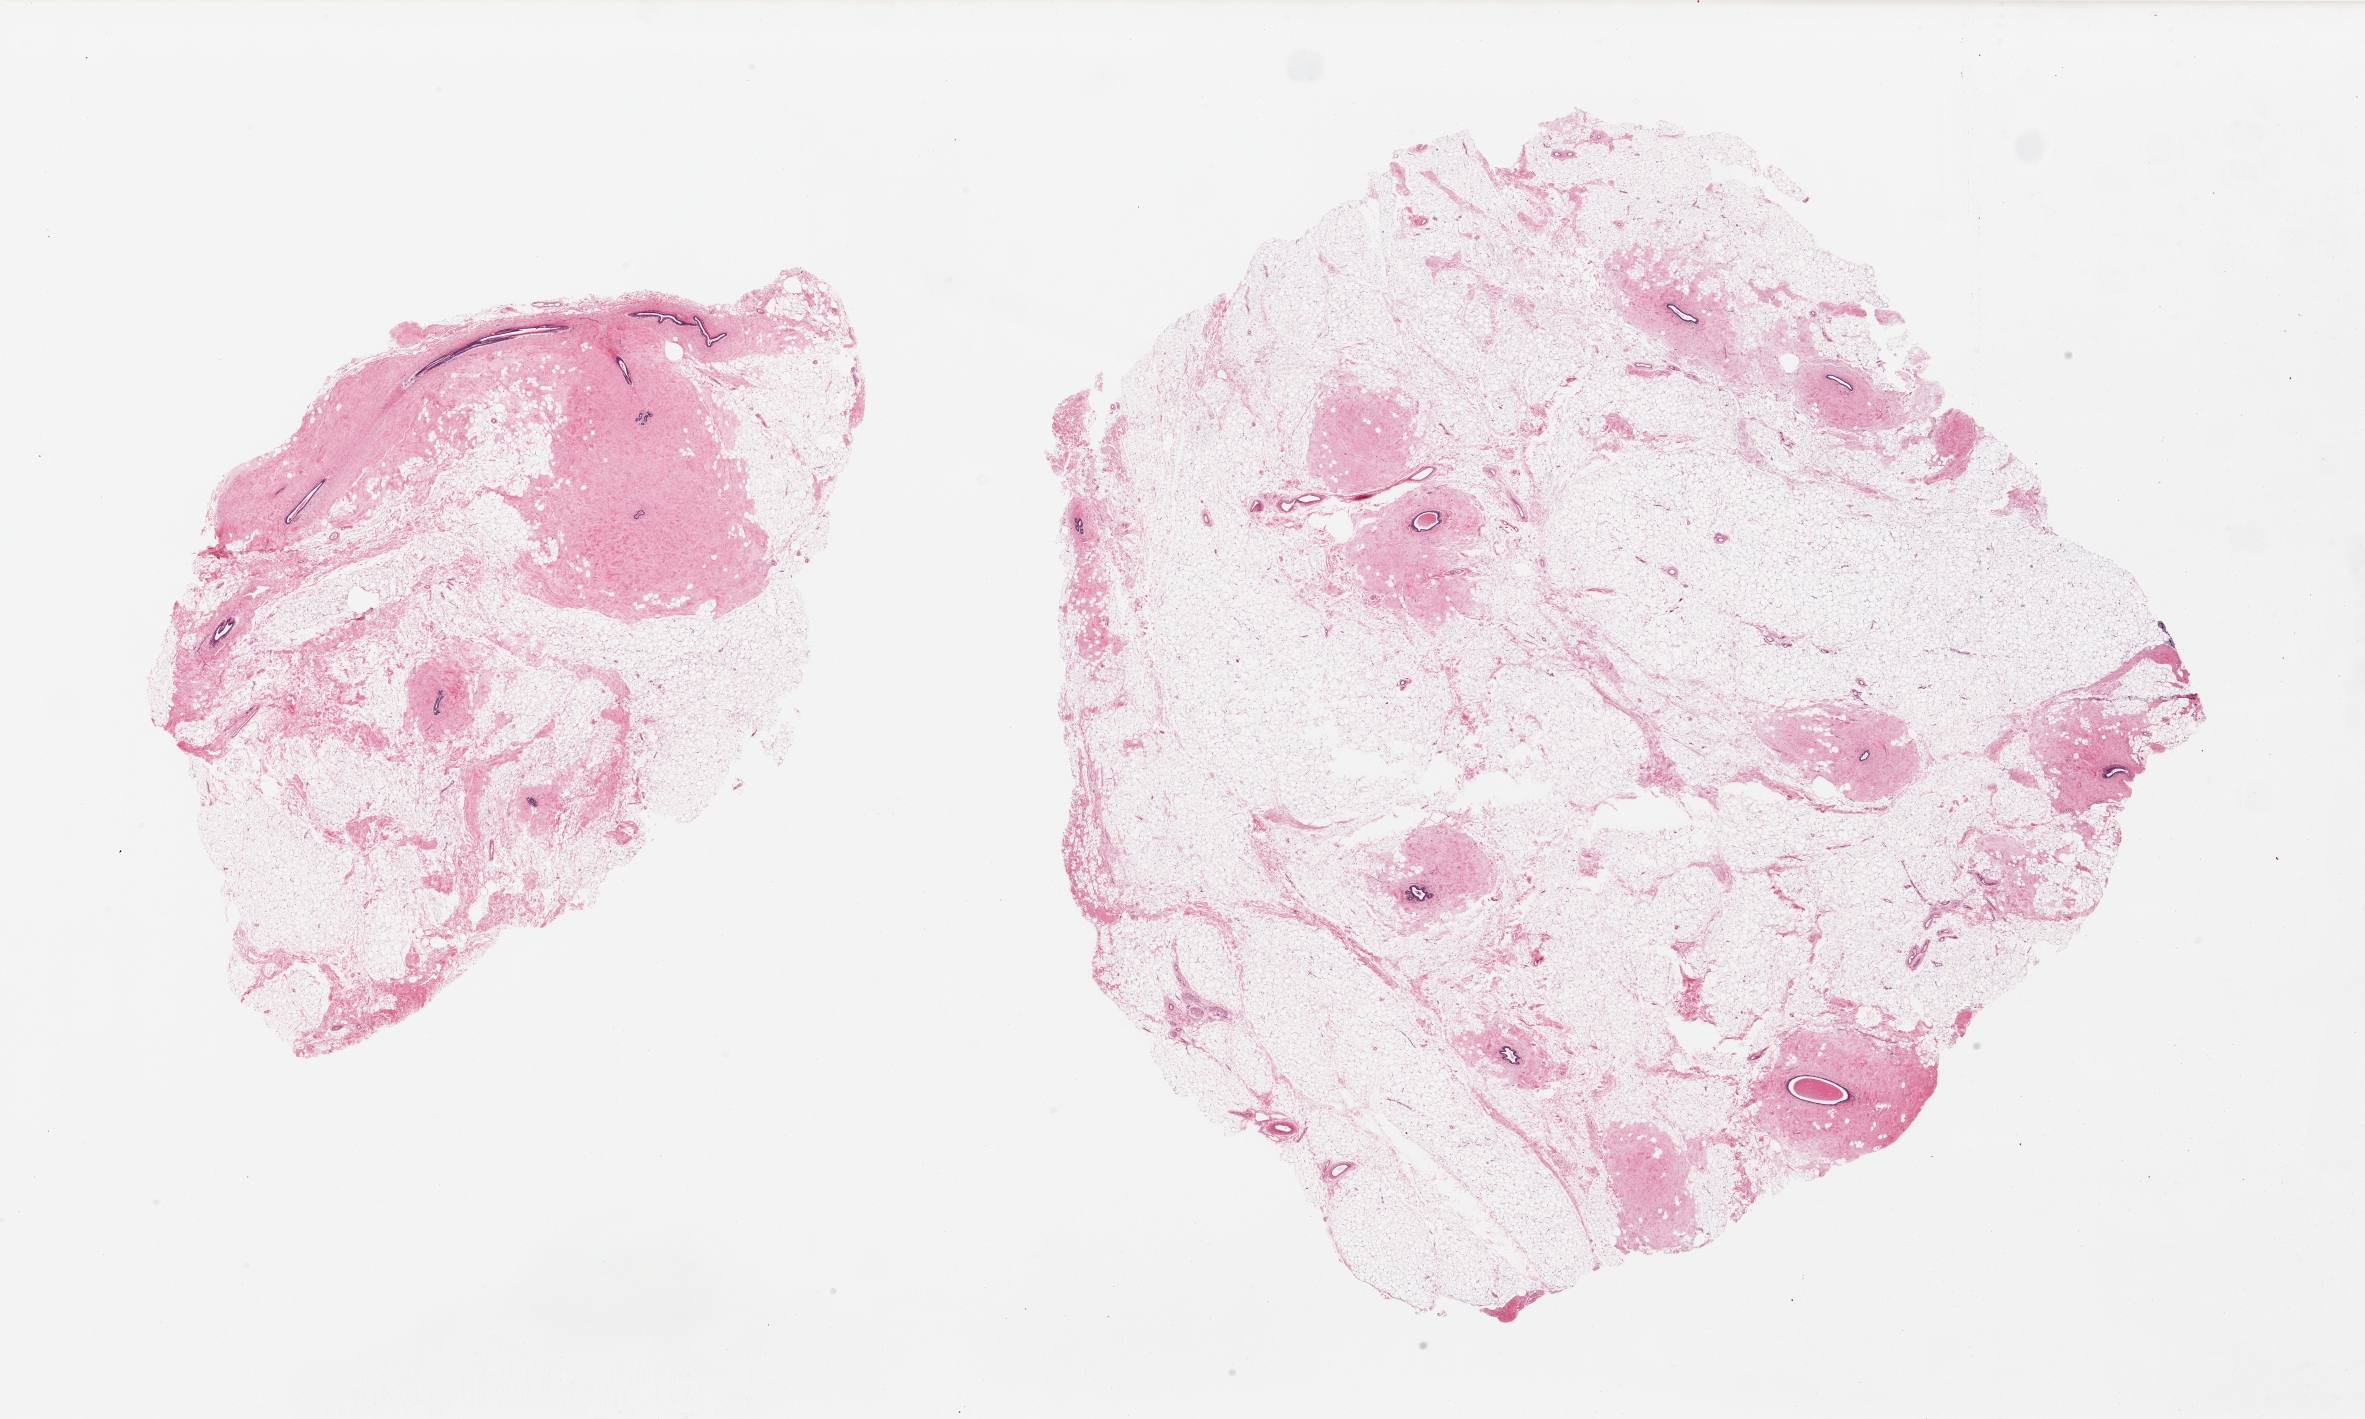
H&E whole-slide image — shown as a low-resolution overview of the whole scanned area (about 37.4 x 22.4 mm, slide scanned at 20x). PAXgene-fixed, paraffin-embedded tissue. Target tissue: breast. Donor tissue sample. Donor sex: female.
• pathologist's review note for this sample: 2 pieces, smaller is 70% fat, larger is 90% fat; epithelial component is <5%, focal microcalcification and fibrosis